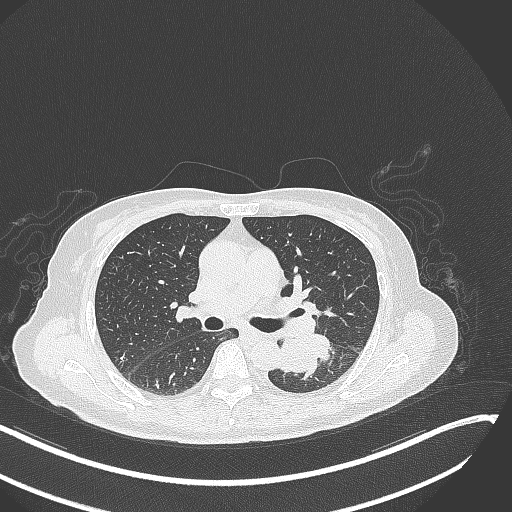
Chest CT, one axial slice; slice 167 of 342 in the series (ordered by position); 120 kVp; lung window (W 1500 / L -600 HU); 1 mm slice thickness; 512 × 512 image matrix, field of view 400 × 400 mm. Patient: female, 64 years. Case-level facts recorded for this patient, not image findings: clinical TNM (as recorded): T3 N1 M1; histopathological grade: G3.
Outlined on this slice (bounding box drawn by a radiologist):
- lung tumour (recorded histology: small cell carcinoma): bounding box <279,334,337,381> (left, top, right, bottom; pixels)